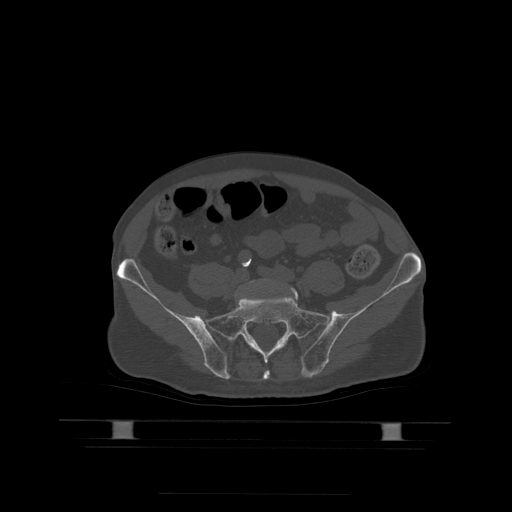
CT including the spine, one axial slice; position 55 of 522 along the scan axis; bone window (W 1800 / L 400 HU); 1.25 mm slice thickness; 512 × 512 image matrix, field of view 436 × 436 mm. Patient age 68 years. From the clinical record (not read from this slice): primary cancer: urothelial.
Outlined on this slice (semi-automatically segmented with operator editing):
- L5 vertebra: bounding box [x1, y1, x2, y2] px = [239, 279, 299, 299]